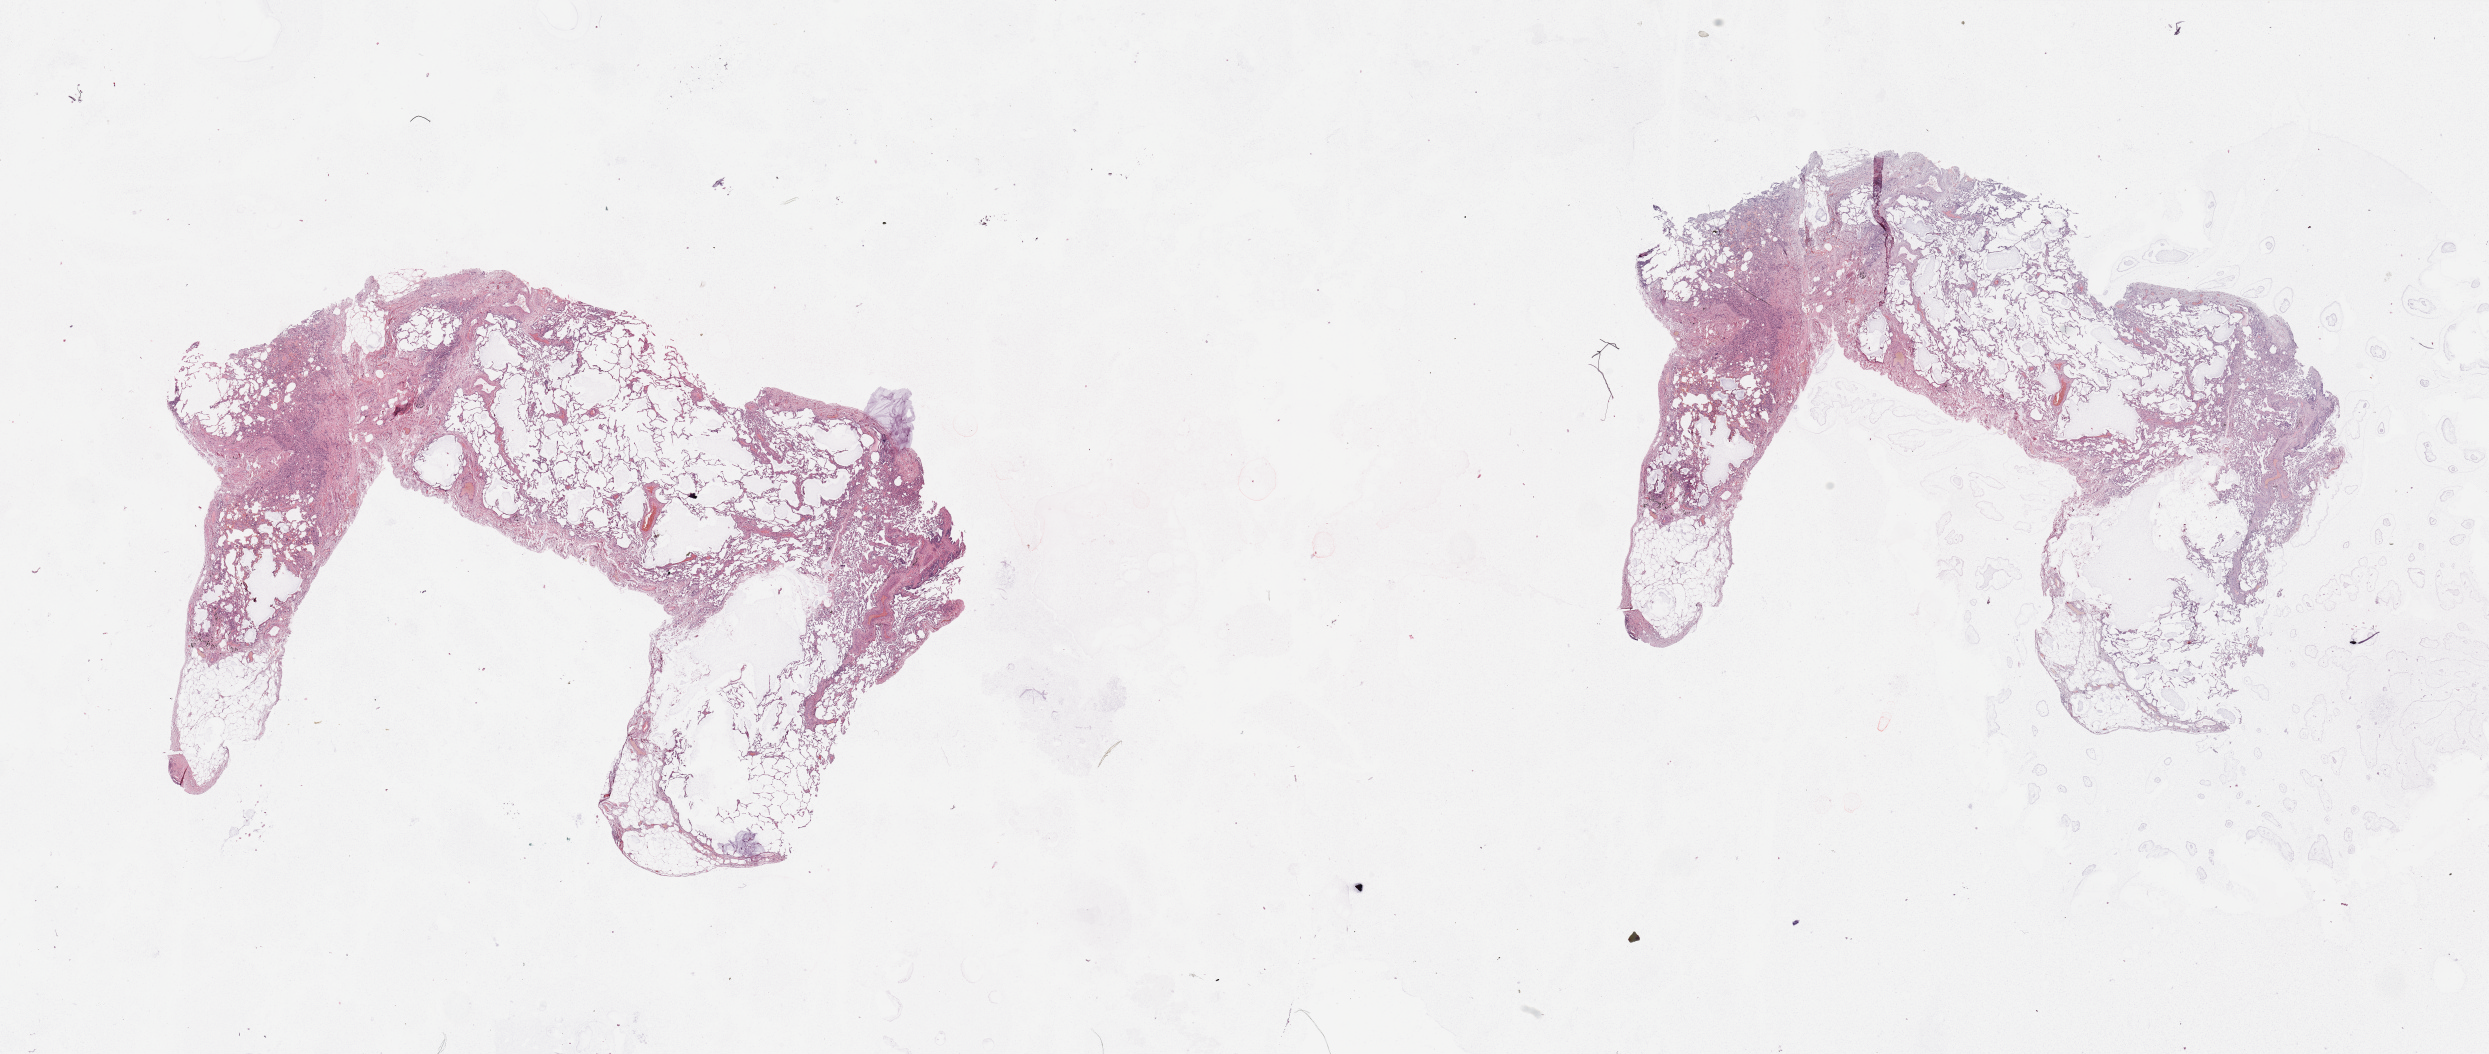
Digitized H&E-stained tissue section (whole slide), low-resolution overview of the scanned area, about 39.4 x 16.7 mm. Normal (non-tumour) tissue sample, sampled site: lung. Patient: male, age 67 years.
- this section: normal (non-tumour) tissue from the same patient
- patient diagnosis: Adenocarcinoma, NOS